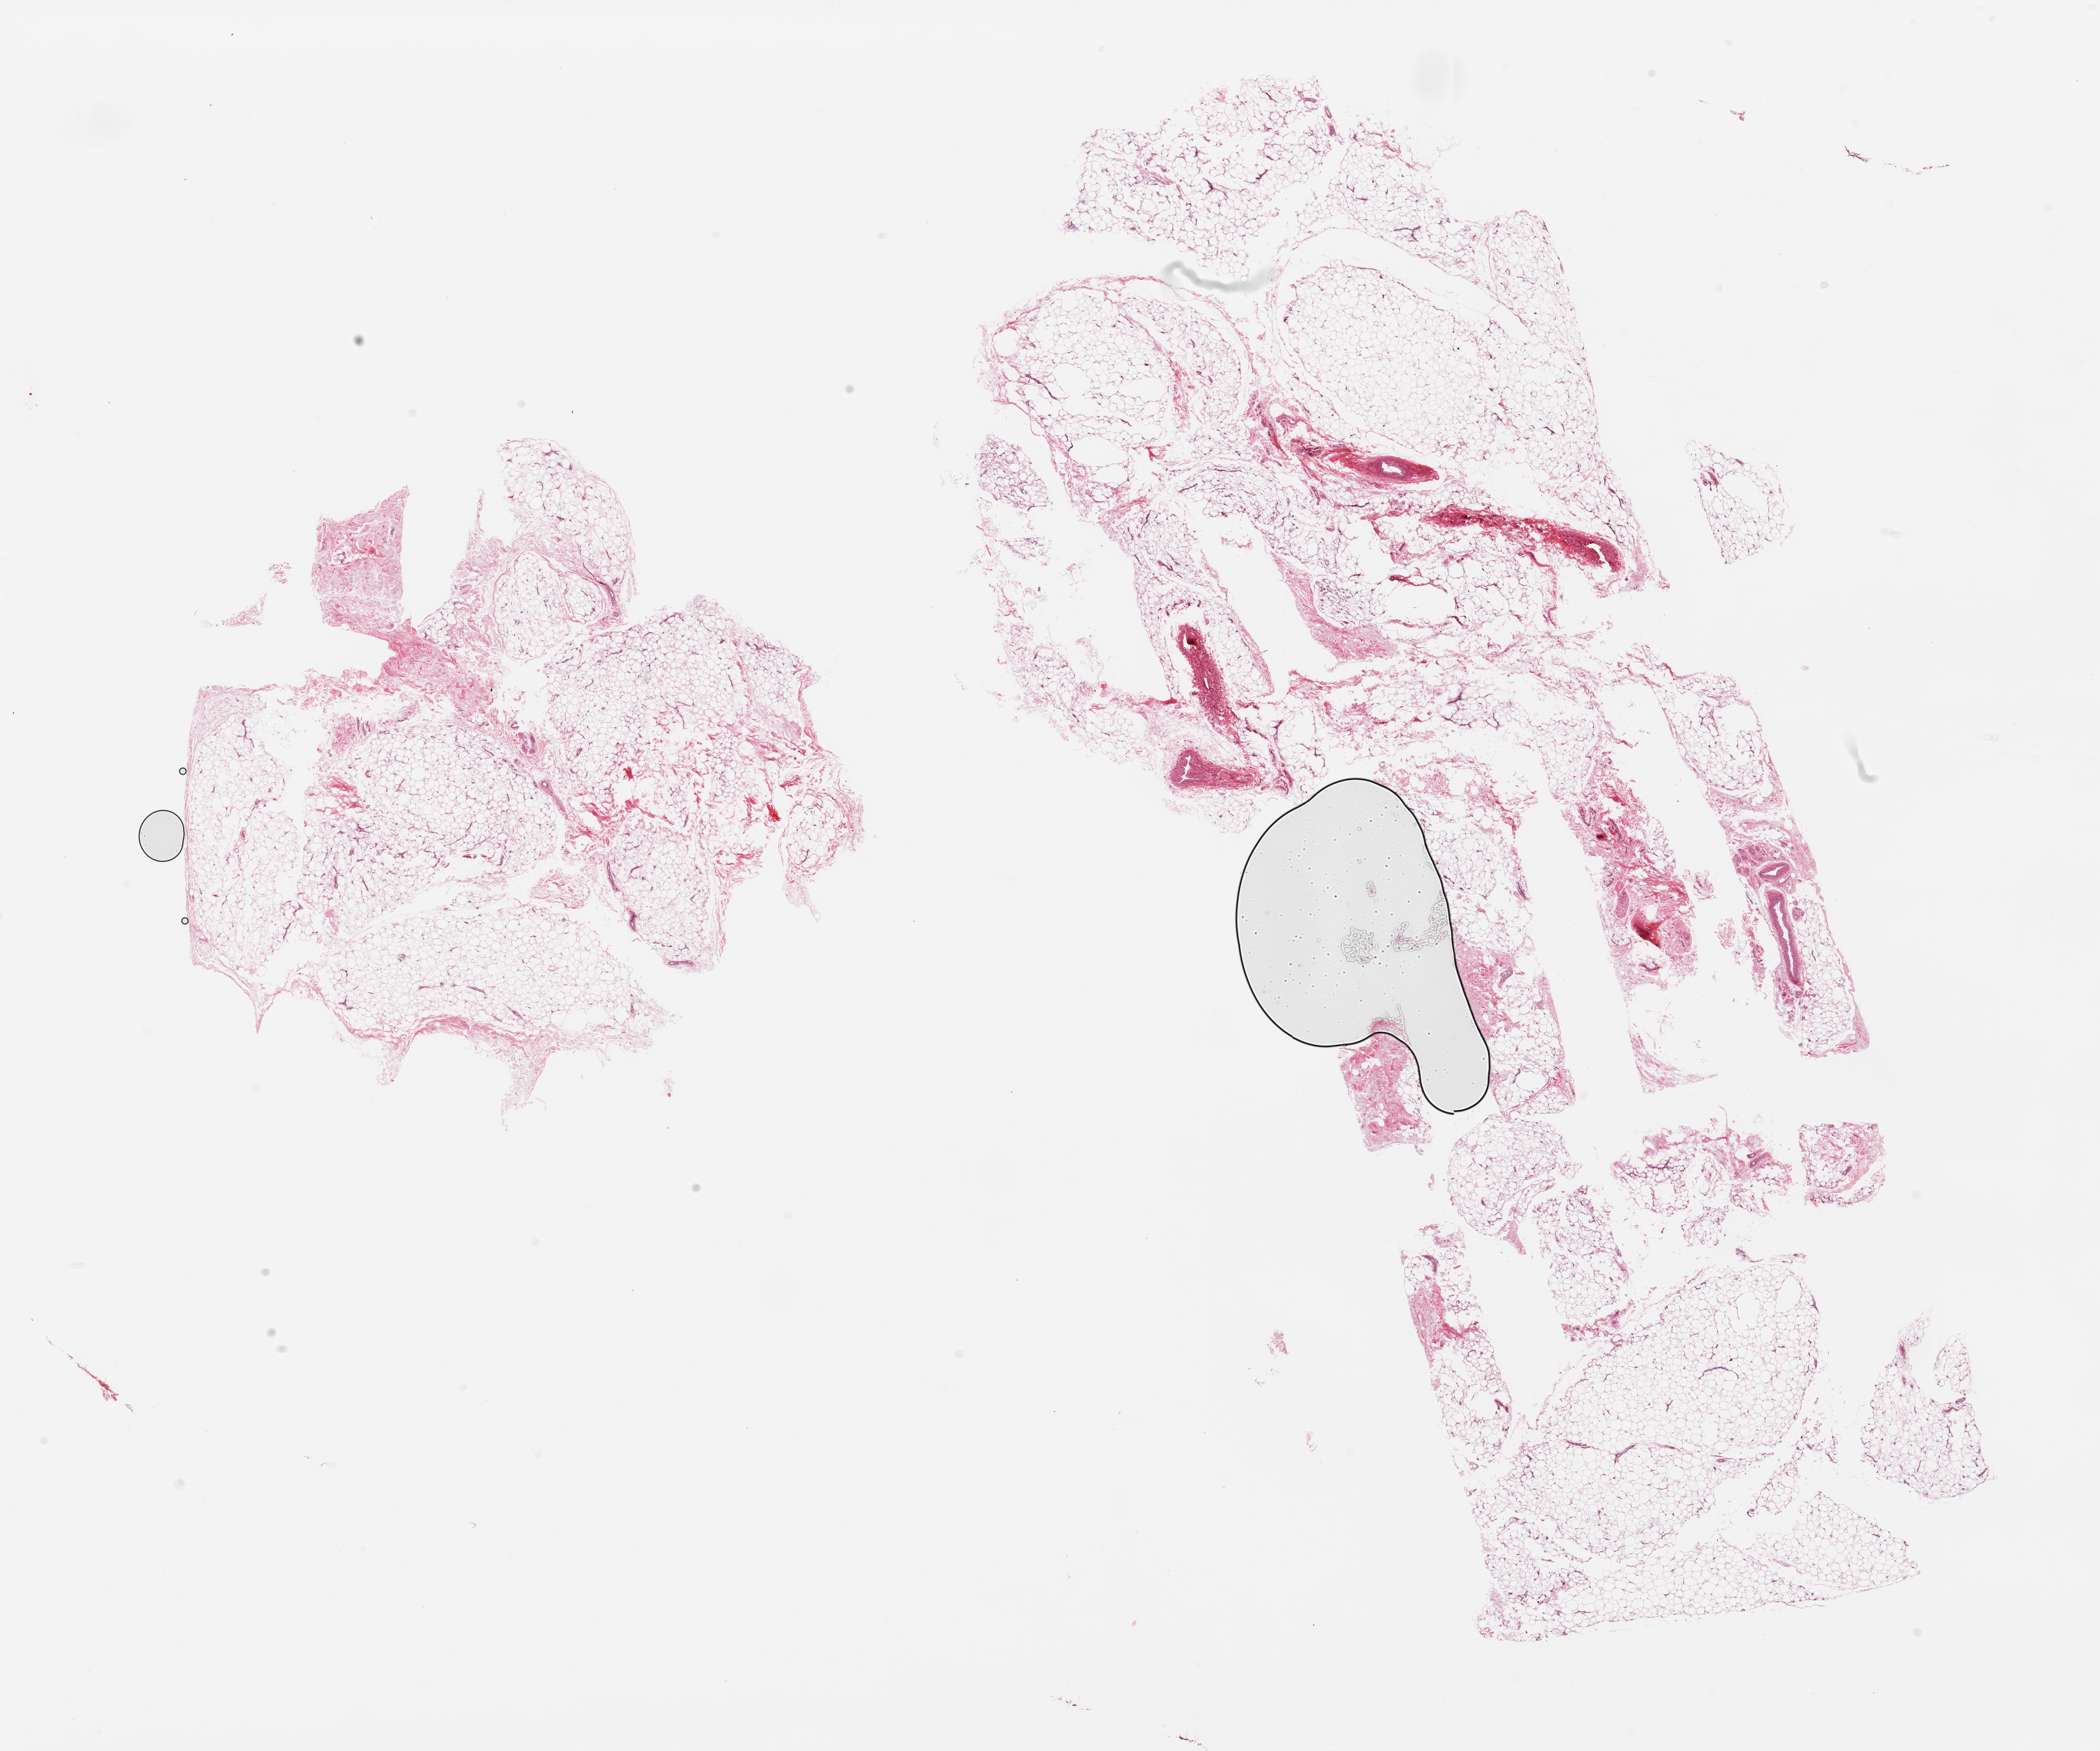
H&E whole-slide image — shown as a low-resolution overview of the whole scanned area (about 25.6 x 21.3 mm); PAXgene-fixed, paraffin-embedded tissue; target tissue: adipose tissue; donor tissue sample. Male donor.
* pathologist's review note for this sample: 2 pieces; overly large specimen with compression artifacts